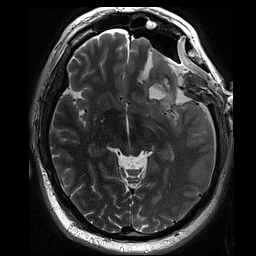
Brain MRI from a brain-tumour surgery series, one axial slice. Position 48 of 70 along the scan axis. 256 × 256 image matrix. Case-level facts recorded for this patient, not image findings: histopathology: Oligodendroglioma; WHO grade: 3; IDH mutation: yes; tumour location: Left Sylvian Fissure (Temporal).
Structures marked on this image (outlined manually by an expert reader):
- residual tumour: box from (x=154, y=84) to (x=176, y=104) px